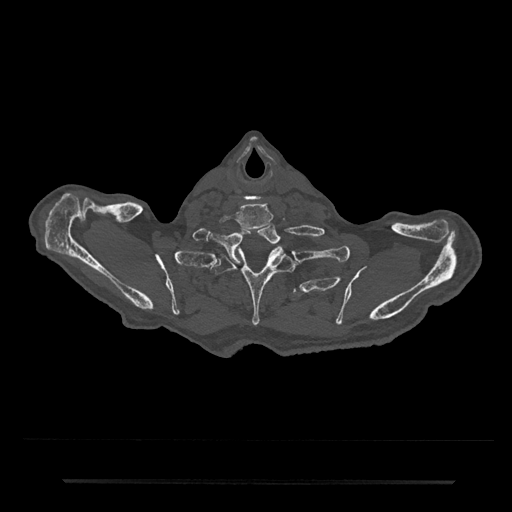
CT including the spine, one axial slice; slice 708 of 797 in the series (ordered by position); reconstruction kernel Br40s/3; bone window (W 1800 / L 400 HU); 0.5 mm slice thickness; 512 × 512 image matrix, field of view 427 × 427 mm. Patient: male, 74 years. Case-level facts recorded for this patient, not image findings: primary cancer: prostate.
Structures marked on this image (semi-automatically segmented with operator editing):
- T1 vertebra: bounding box [x1, y1, x2, y2] px = [218, 222, 284, 264]
- T2 vertebra: [210, 247, 299, 326]
- T3 vertebra: [291, 288, 300, 297]